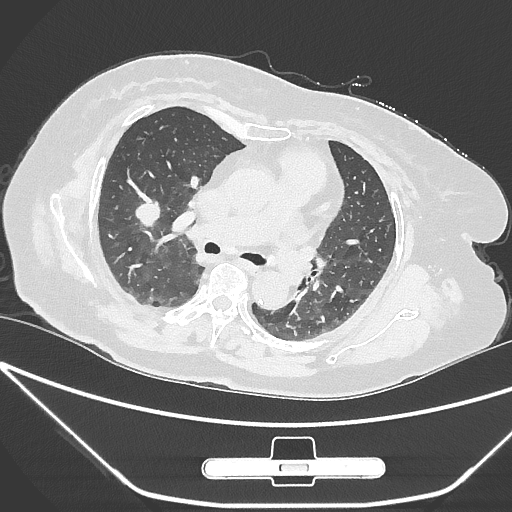
Chest CT, one axial slice. Slice 160 of 245 in the series (ordered by position). Reconstruction kernel IMR1,SharpPlus. Lung window (W 1500 / L -600 HU). 1 mm slice thickness. 512 × 512 image matrix, field of view 365 × 365 mm. Female patient, age 65 years. From the clinical record (not read from this slice): clinical TNM (as recorded): T1c N0 M0; histopathological grade: G3.
Annotated regions visible in this slice (bounding box drawn by a radiologist):
- lung tumour (recorded histology: adenocarcinoma): bounding box (x1, y1, x2, y2) in pixels: (129, 194, 180, 245)